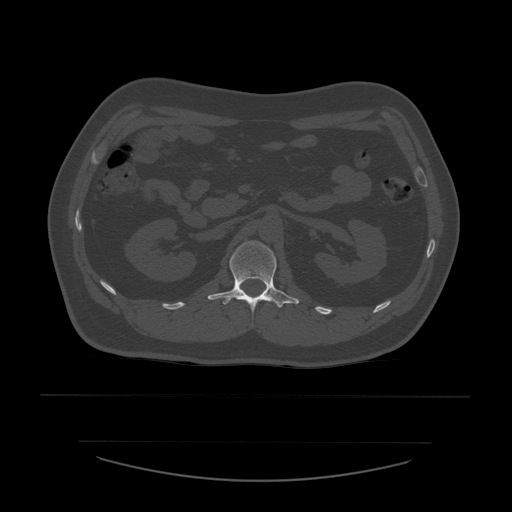
CT including the spine, one axial slice. Position 226 of 532 along the scan axis. Reconstruction kernel STANDARD. Bone window (W 1800 / L 400 HU). 1.25 mm slice thickness. 512 × 512 image matrix, field of view 441 × 441 mm. Patient age 44 years. From the clinical record (not read from this slice): primary cancer: soft tissue sarcoma.
Annotated regions visible in this slice (semi-automatically segmented with operator editing):
- L1 vertebra: bounding box <208,241,299,312> (left, top, right, bottom; pixels)